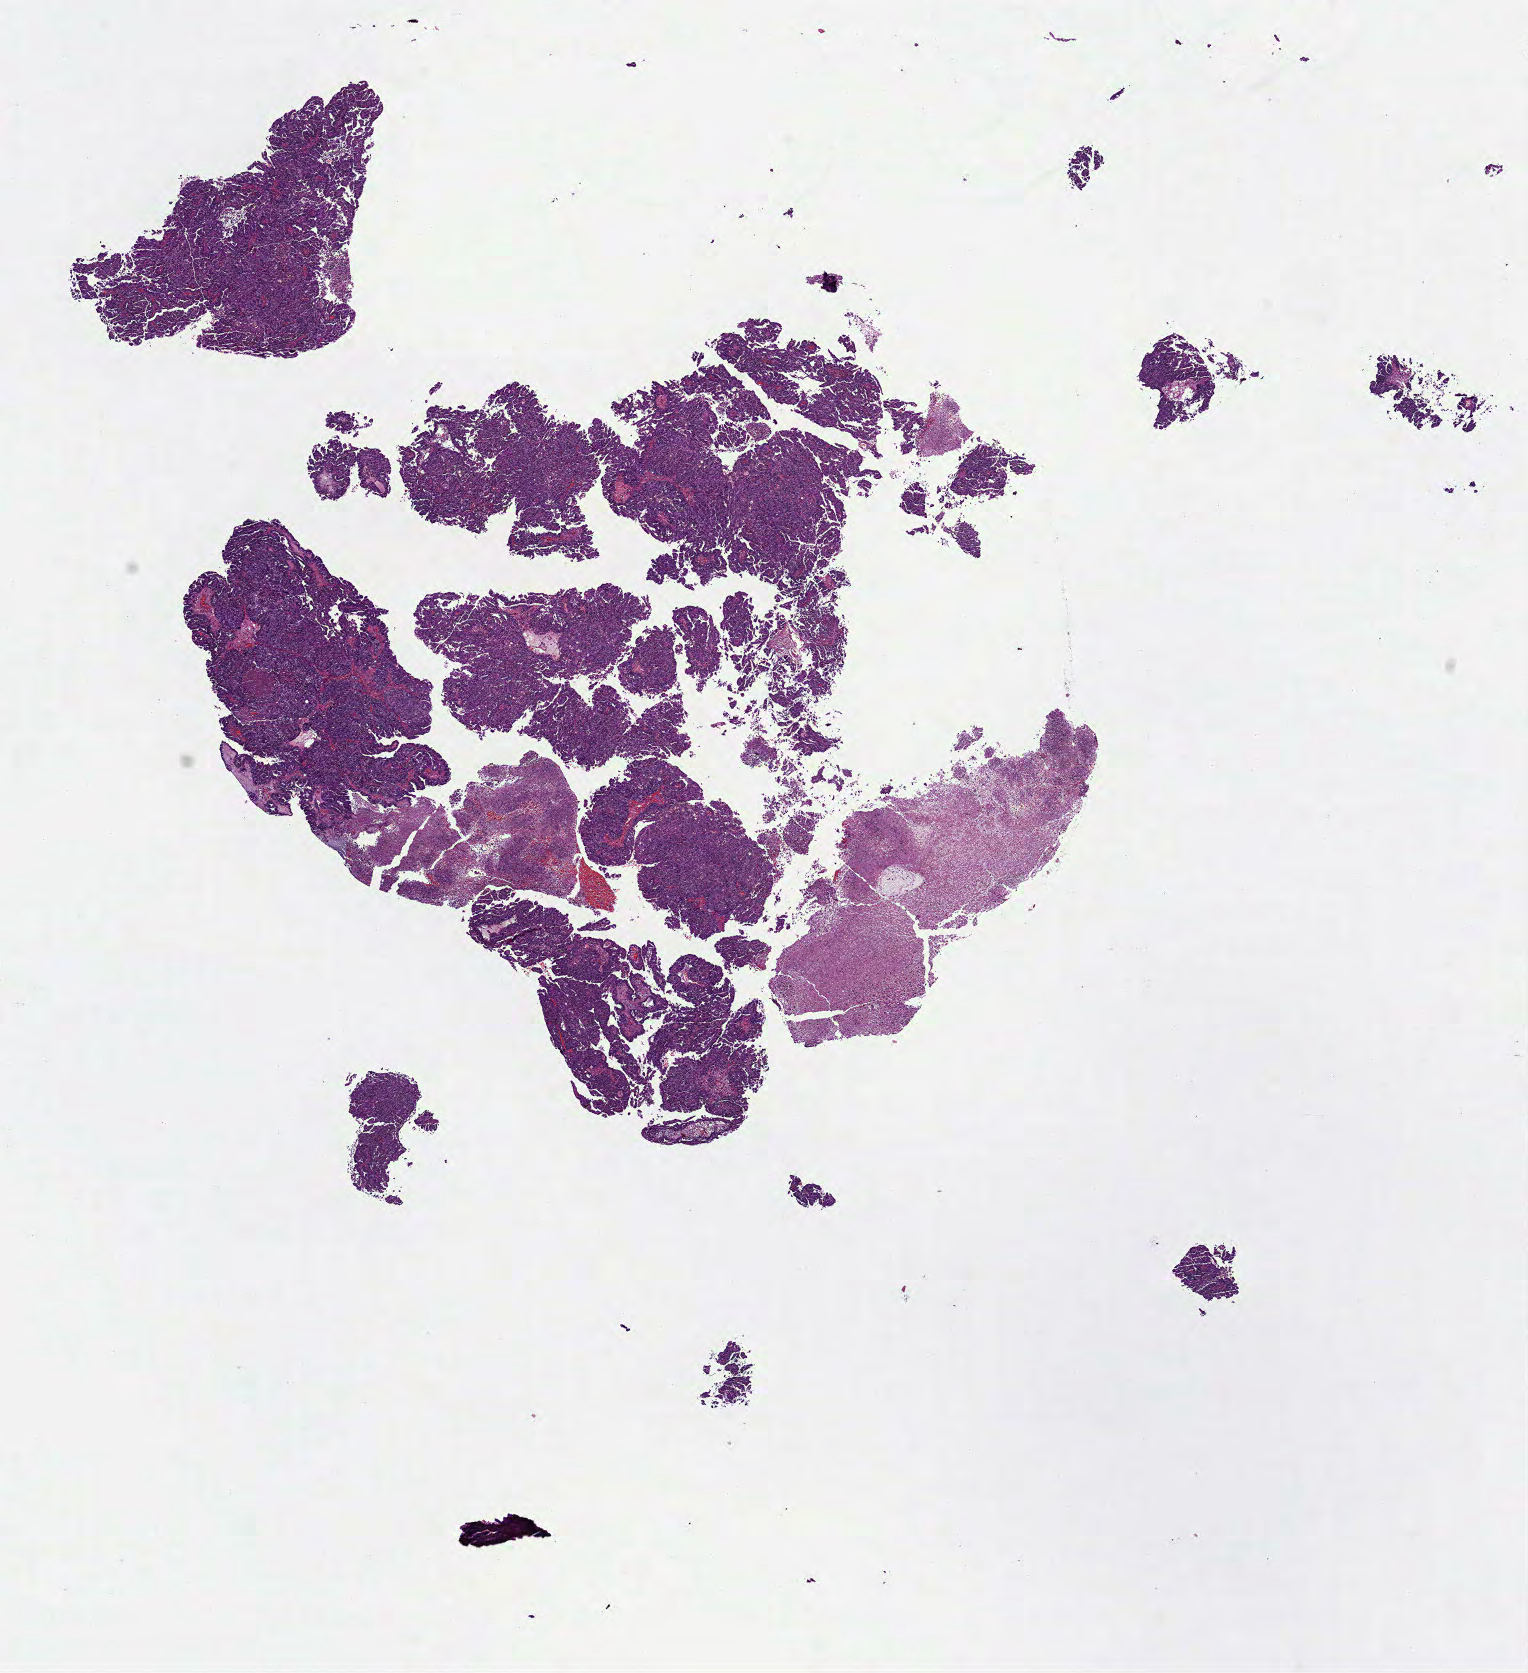
H&E-stained whole-slide image — shown as a low-resolution overview of the whole scanned area (about 12.3 x 13.5 mm). FFPE section. Ovary, primary tumour sample. Patient: female, age at initial diagnosis 63 years.
* histologic diagnosis: Serous cystadenocarcinoma, NOS